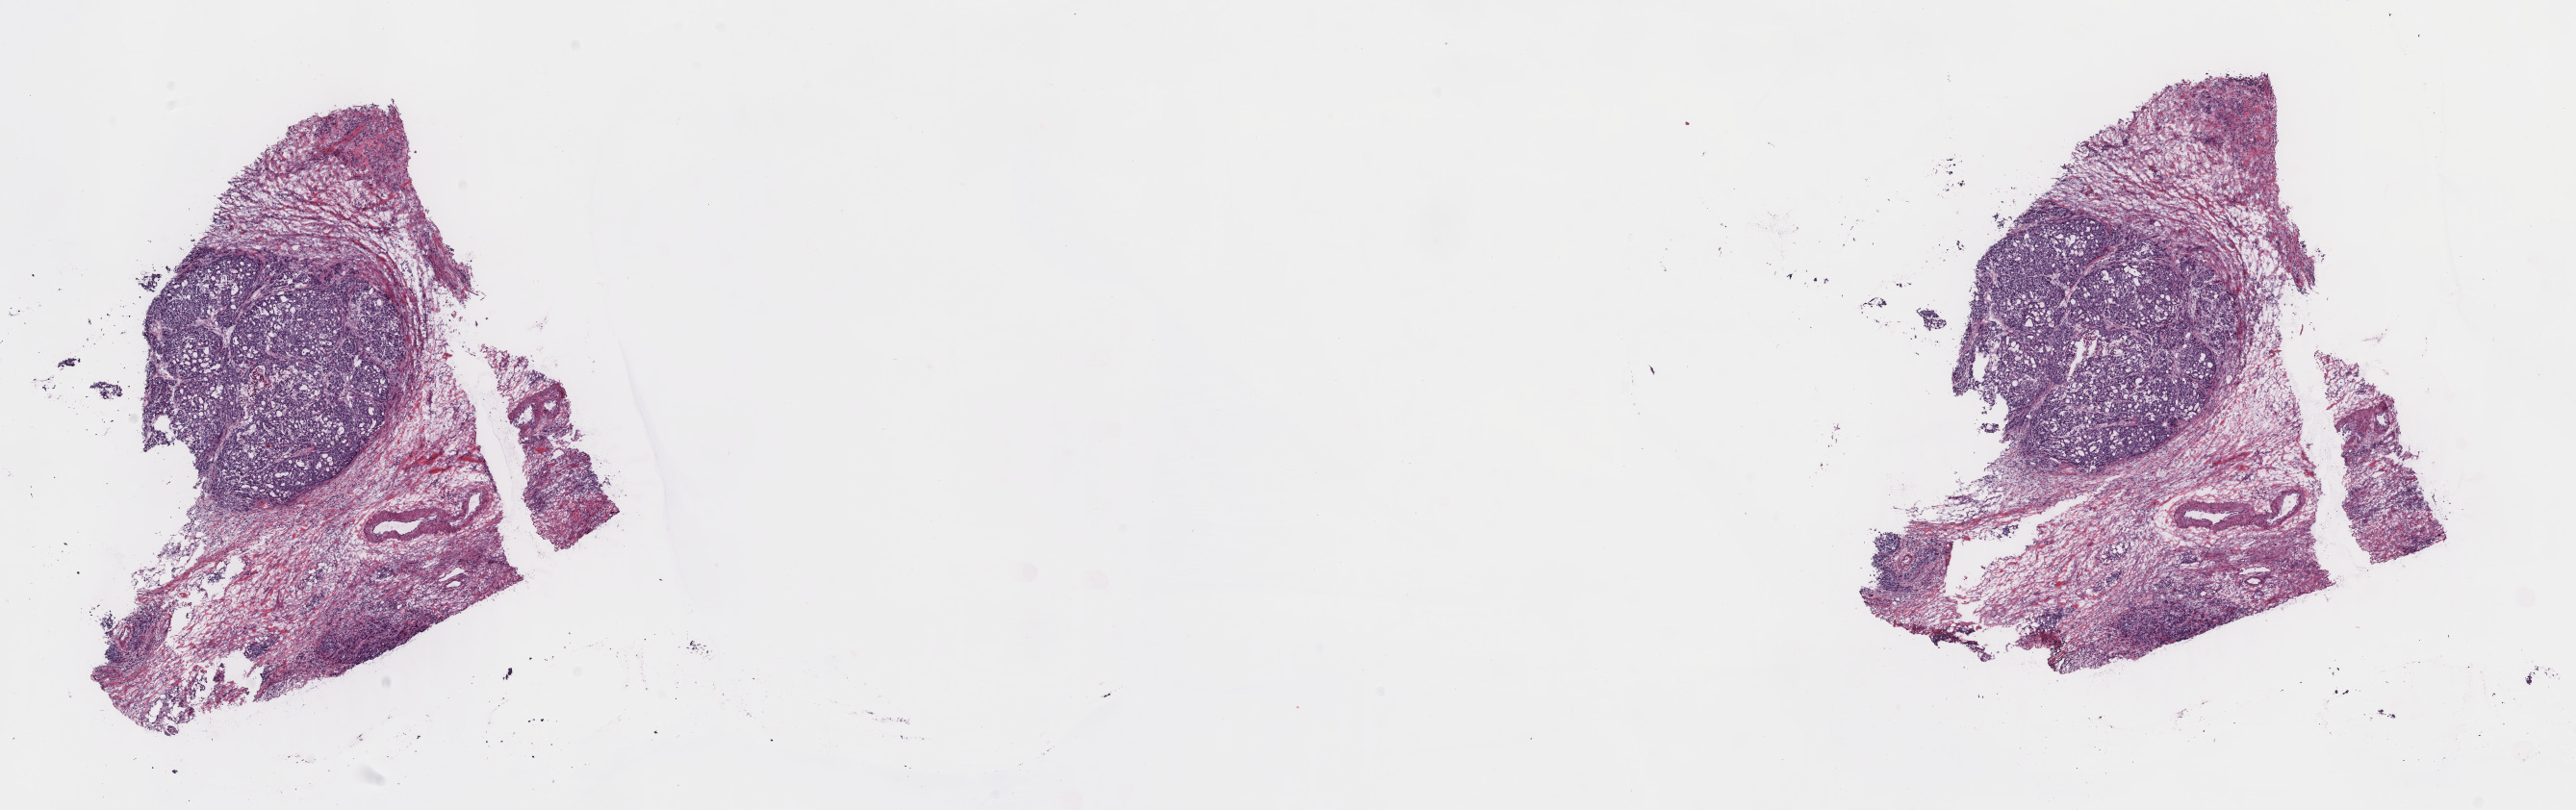
Digitized H&E-stained tissue section (whole slide), a low-resolution overview of the entire scanned area, about 21.2 x 6.7 mm. Frozen section. Primary tumour sample from the stomach. Female, age 79 years at initial diagnosis.
Pathologic diagnosis: Adenocarcinoma, NOS (gastric antrum).